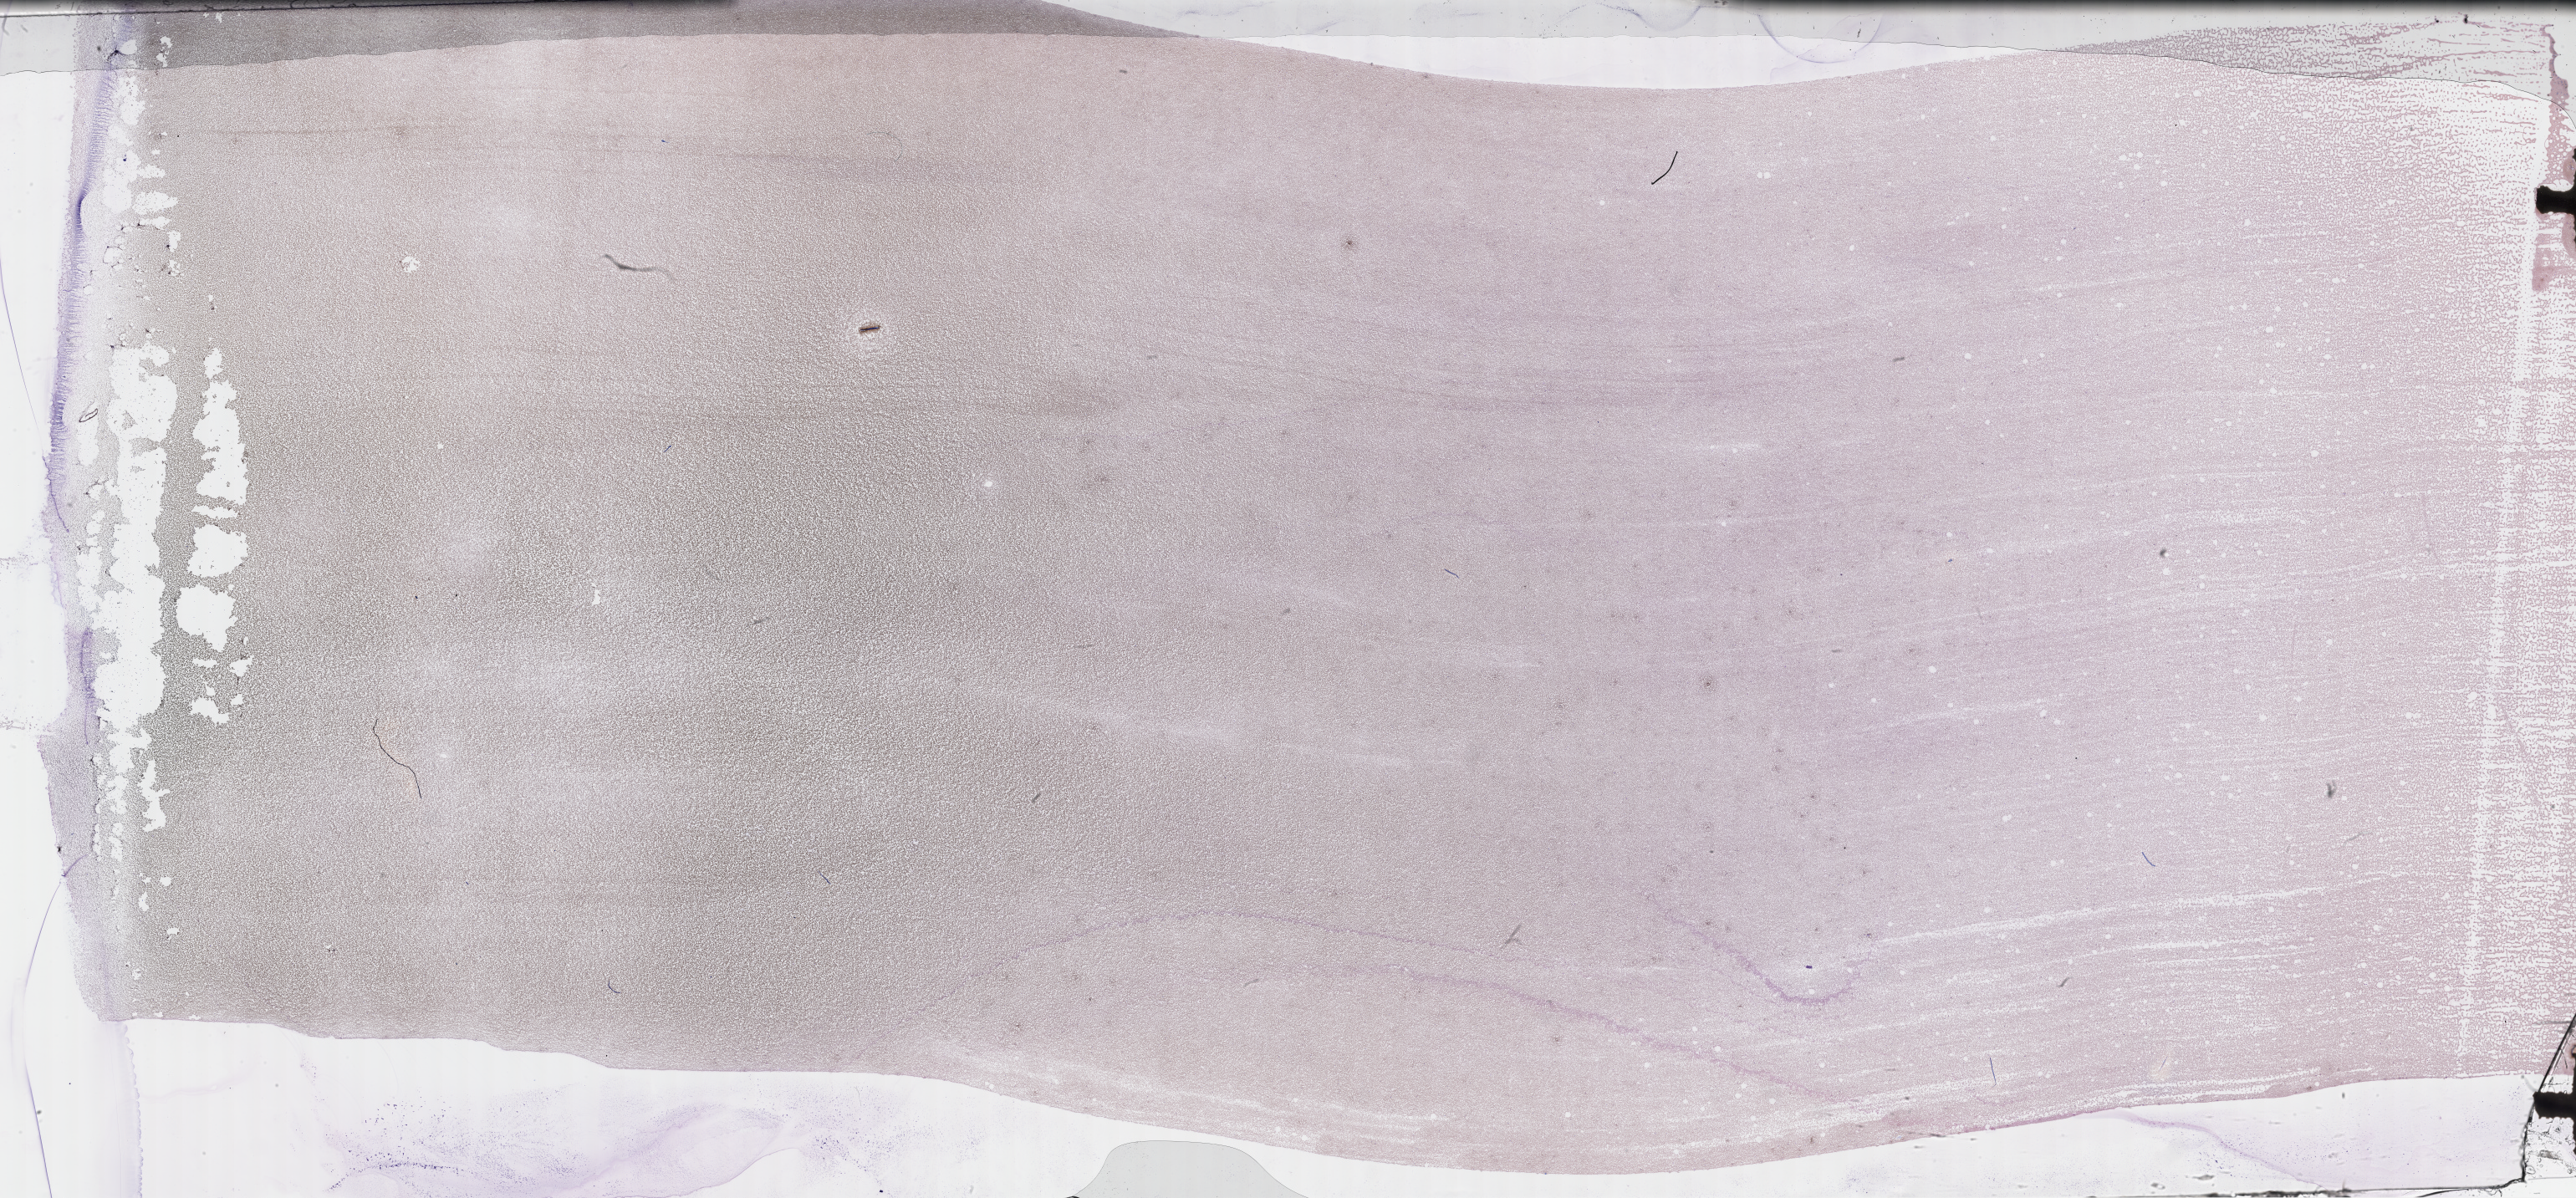
Whole-slide image of a whole blood smear, Wright–Giemsa stain — shown as a low-resolution overview of the whole scanned area (about 49.8 x 23.1 mm); smear from an EDTA sample; specimen time point: collected on treatment. Patient sex: male.
Patient diagnosis: Plasma Cell Myeloma.